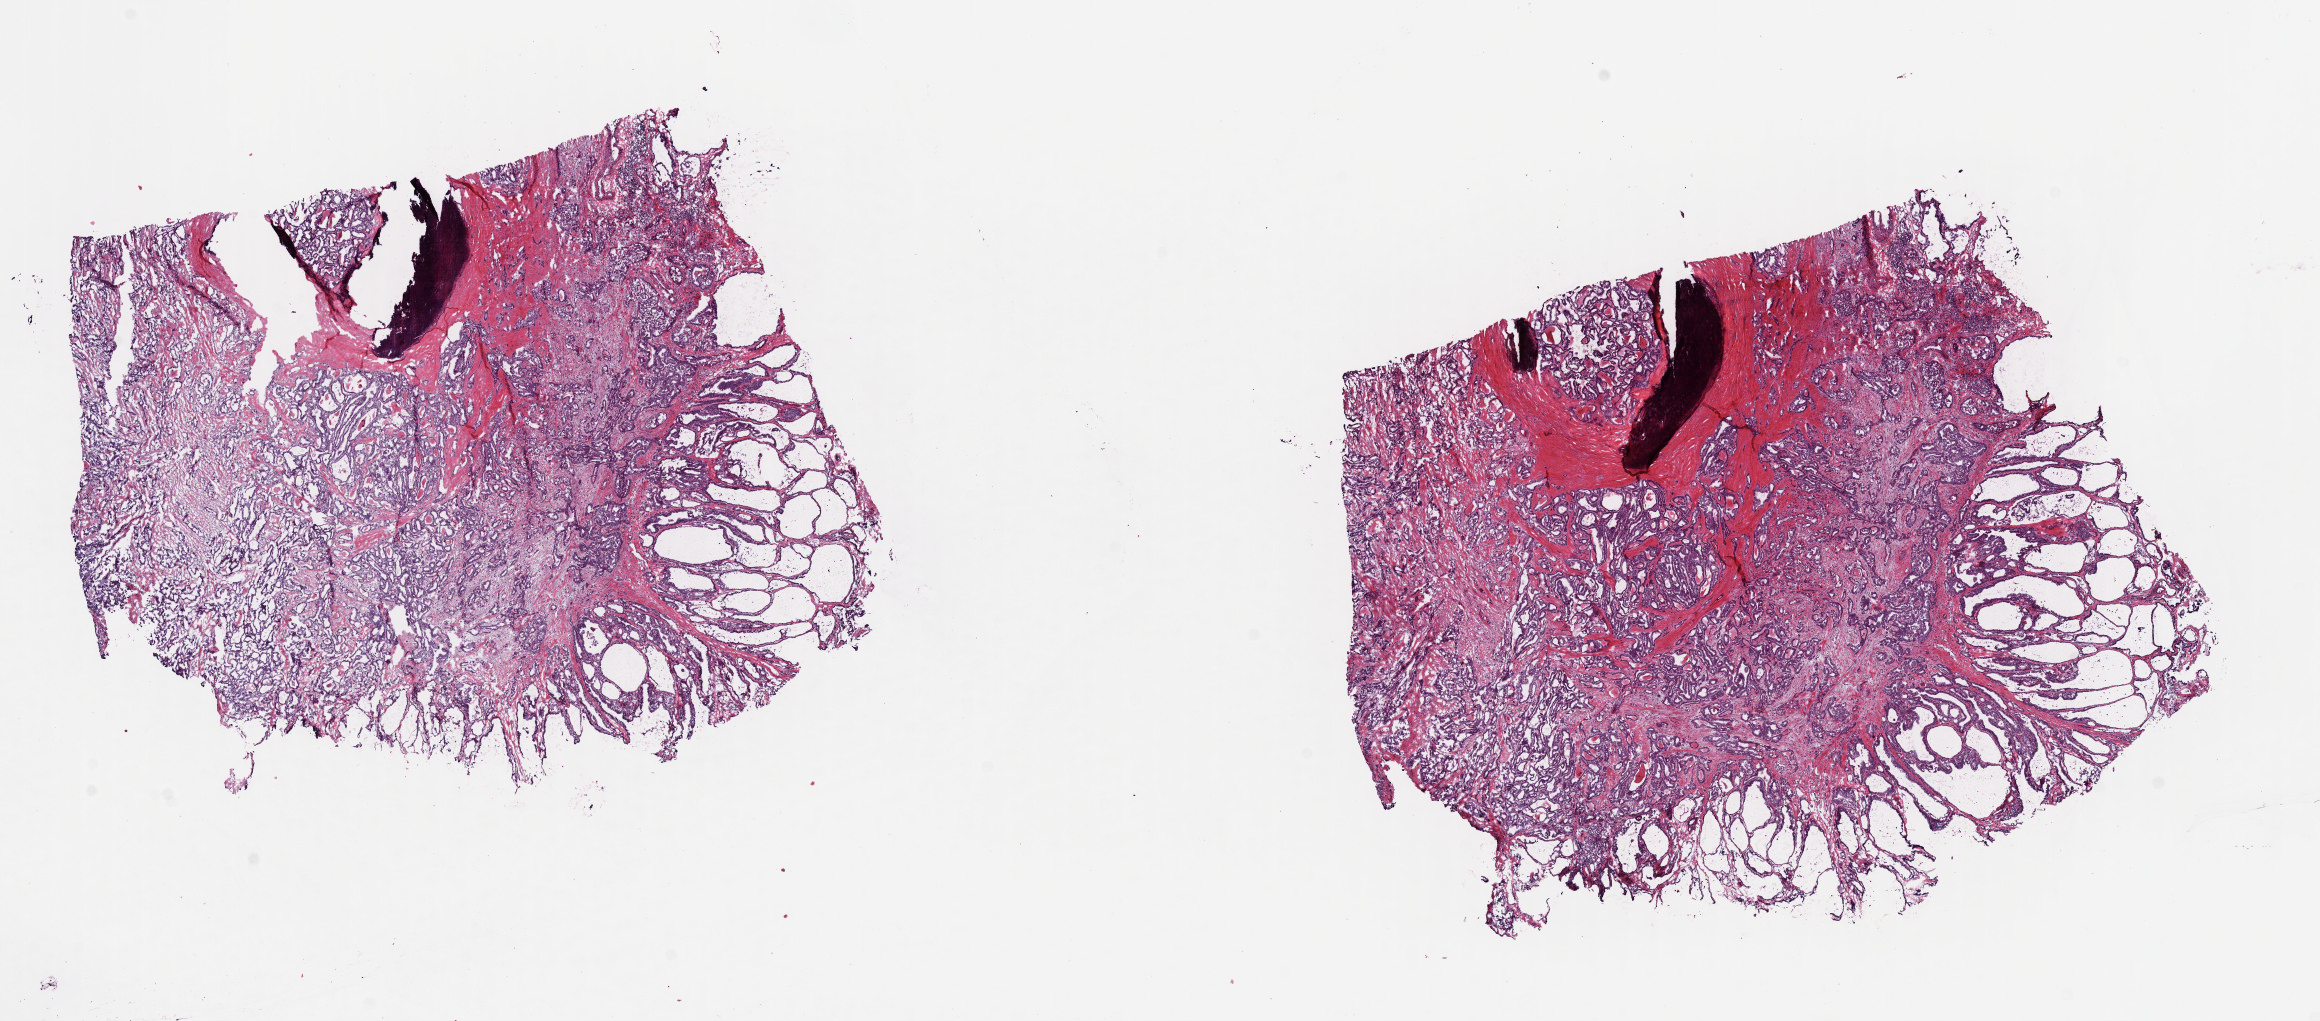
Digitized Hematoxylin and eosin (H&E) stained tissue section (whole slide), a low-resolution overview of the entire scanned area, about 18.3 x 8.1 mm (slide scanned at 40x); frozen section from the top of the tissue portion; primary tumour sample from the thyroid. Male patient; age at initial diagnosis 42 years. Slide review estimates, as recorded: tumour cells 70%, tumour nuclei 70%, normal cells 8%, stromal cells 22%, necrosis 0%. Infiltration values recorded for this section: lymphocyte infiltration 2%, monocyte infiltration 2%, neutrophil infiltration 0%.
- AJCC pathologic stage: I (7th edition)
- lymph nodes positive (case pathology): 0 of 2 examined
- TNM: T1a N0 M0
- pathologic diagnosis: Papillary carcinoma, follicular variant (thyroid gland)